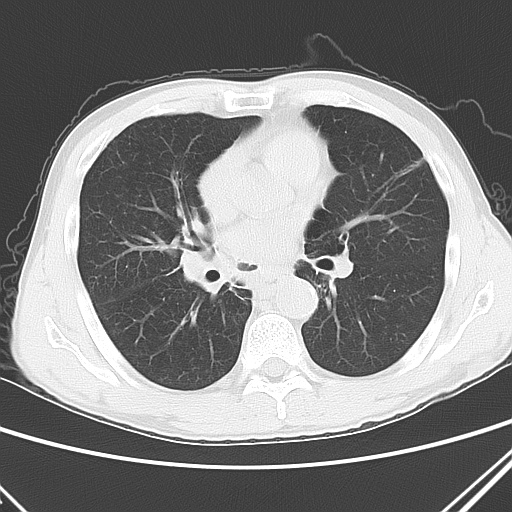
Chest CT, one axial slice. Lung window (W 1500 / L -600 HU). 5 mm slice thickness. 512 × 512 image matrix. Patient: male, 52 years. From the clinical record (not read from this slice): clinical TNM (as recorded): T2a N0 M1c.
Outlined on this slice (bounding box drawn by a radiologist):
- lung tumour (recorded histology: squamous cell carcinoma): bounding box (x1, y1, x2, y2) in pixels: (174, 237, 242, 320)